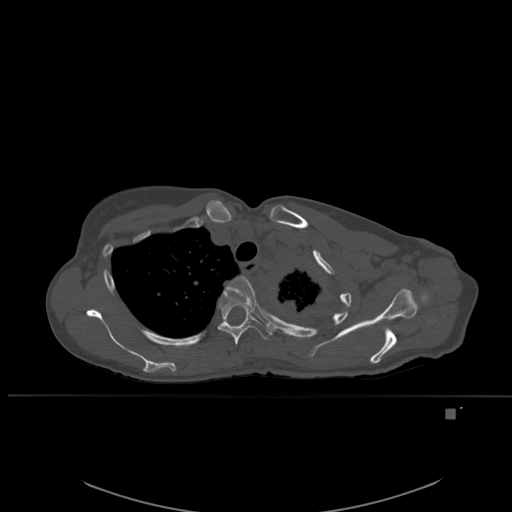
CT including the spine, one axial slice. Slice 415 of 537 in the series (ordered by position). Bone window (W 1800 / L 400 HU). 1.5 mm slice thickness. 512 × 512 image matrix. Female patient, age 45 years. Case-level facts recorded for this patient, not image findings: primary cancer: lung.
Outlined on this slice (semi-automatic segmentation, software-assisted and operator-edited):
- T3 vertebra: bounding box <226,276,256,306> (left, top, right, bottom; pixels)
- T4 vertebra: <218,290,272,346>